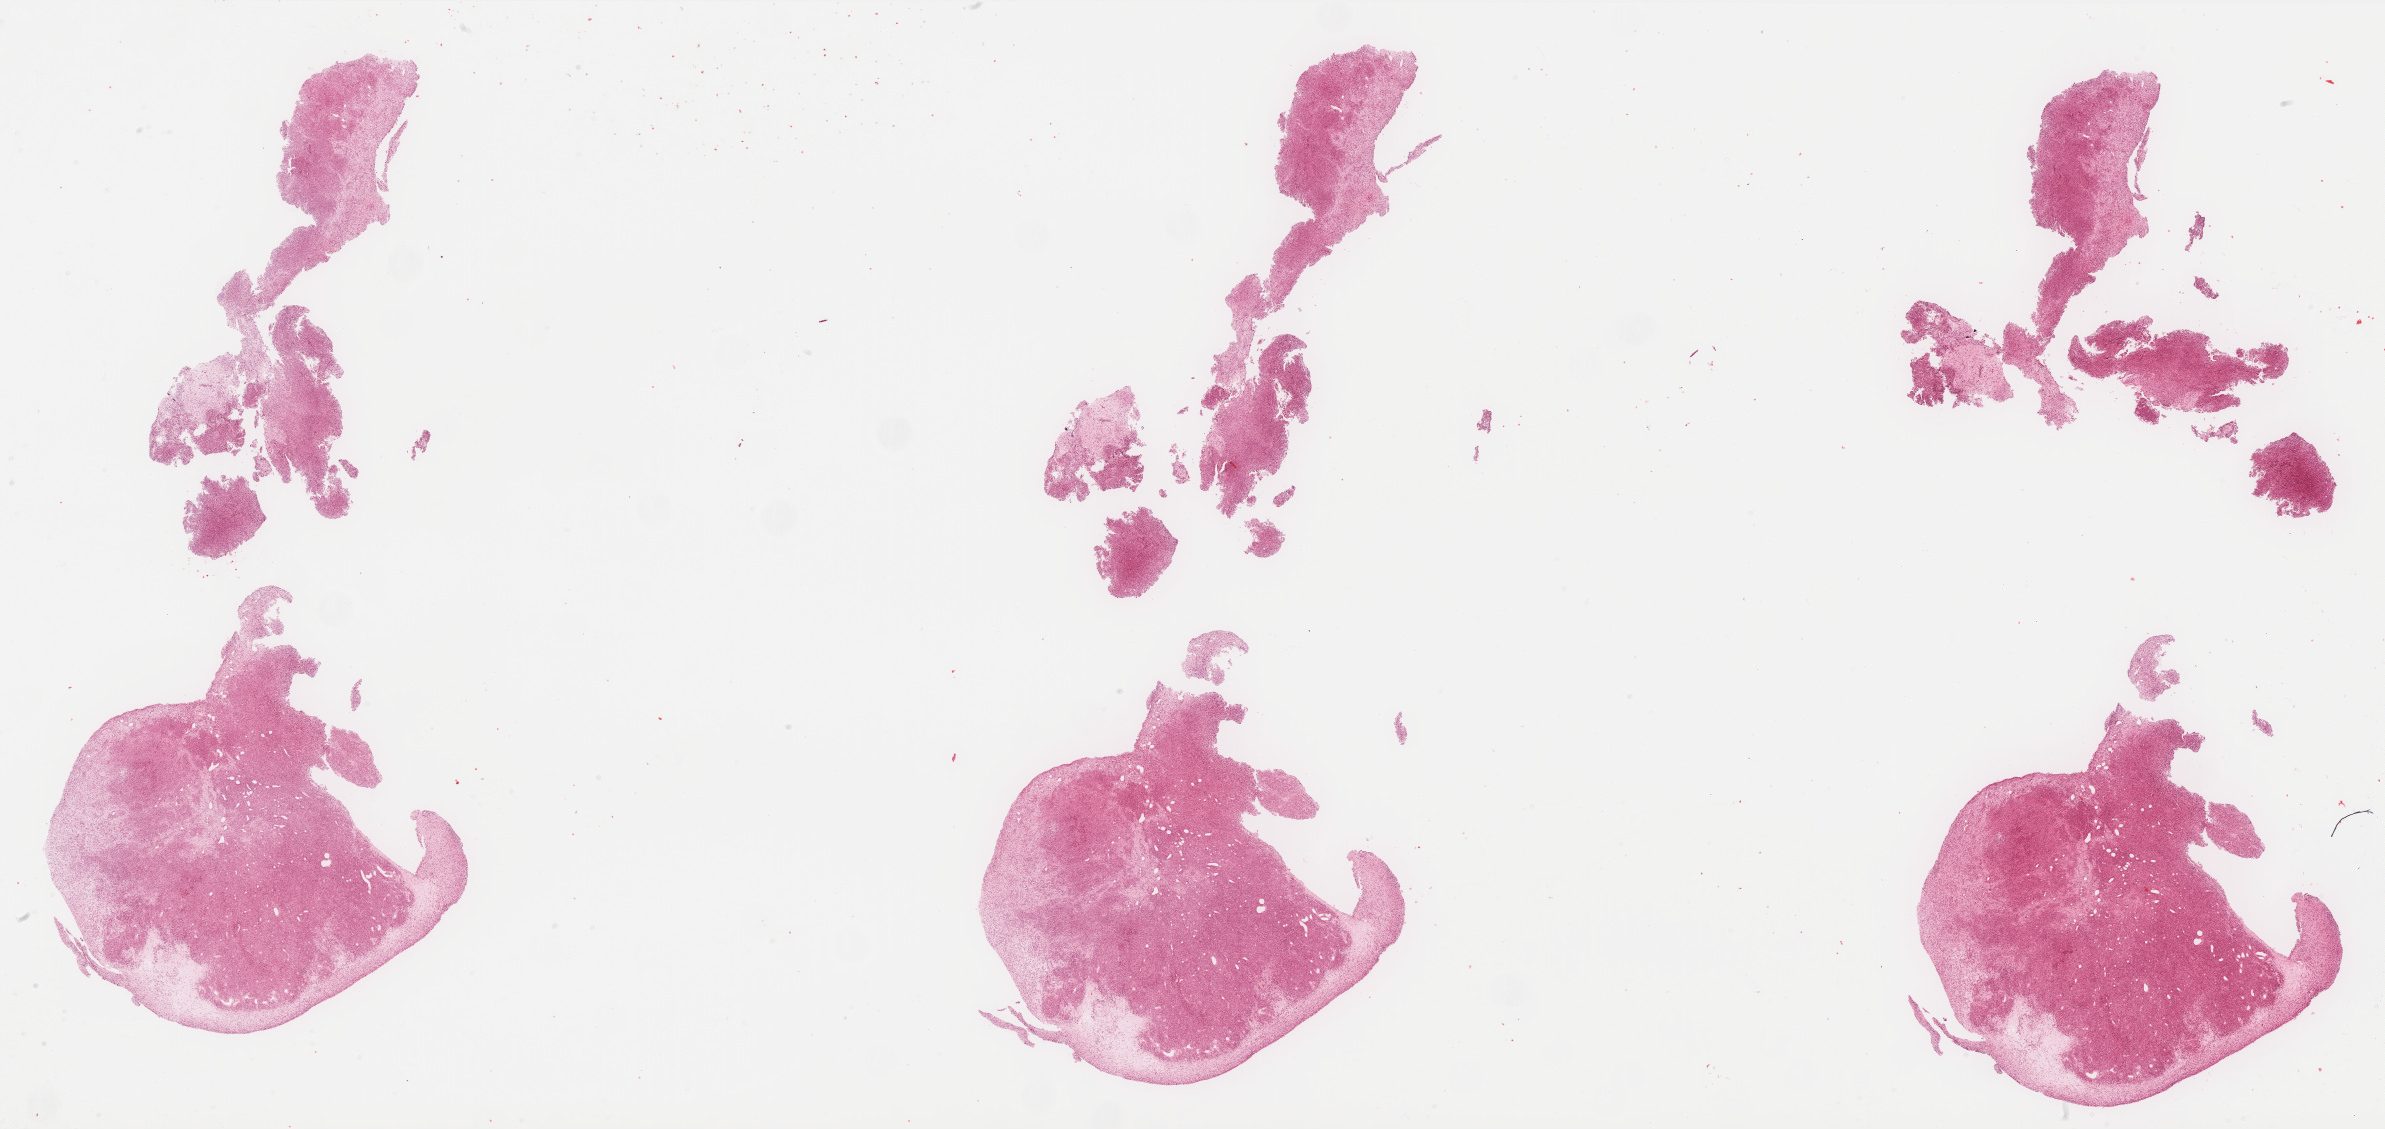
Hematoxylin and eosin (H&E) stained whole-slide image — a low-resolution overview of the entire scanned area, about 38.2 x 18.1 mm (from a 40x scan). FFPE section. Mesothelium, primary tumour sample. Patient: female, age at initial diagnosis 65 years.
- AJCC pathologic stage: III (7th edition)
- pathologic diagnosis: Mesothelioma, biphasic, malignant (pleura, NOS)